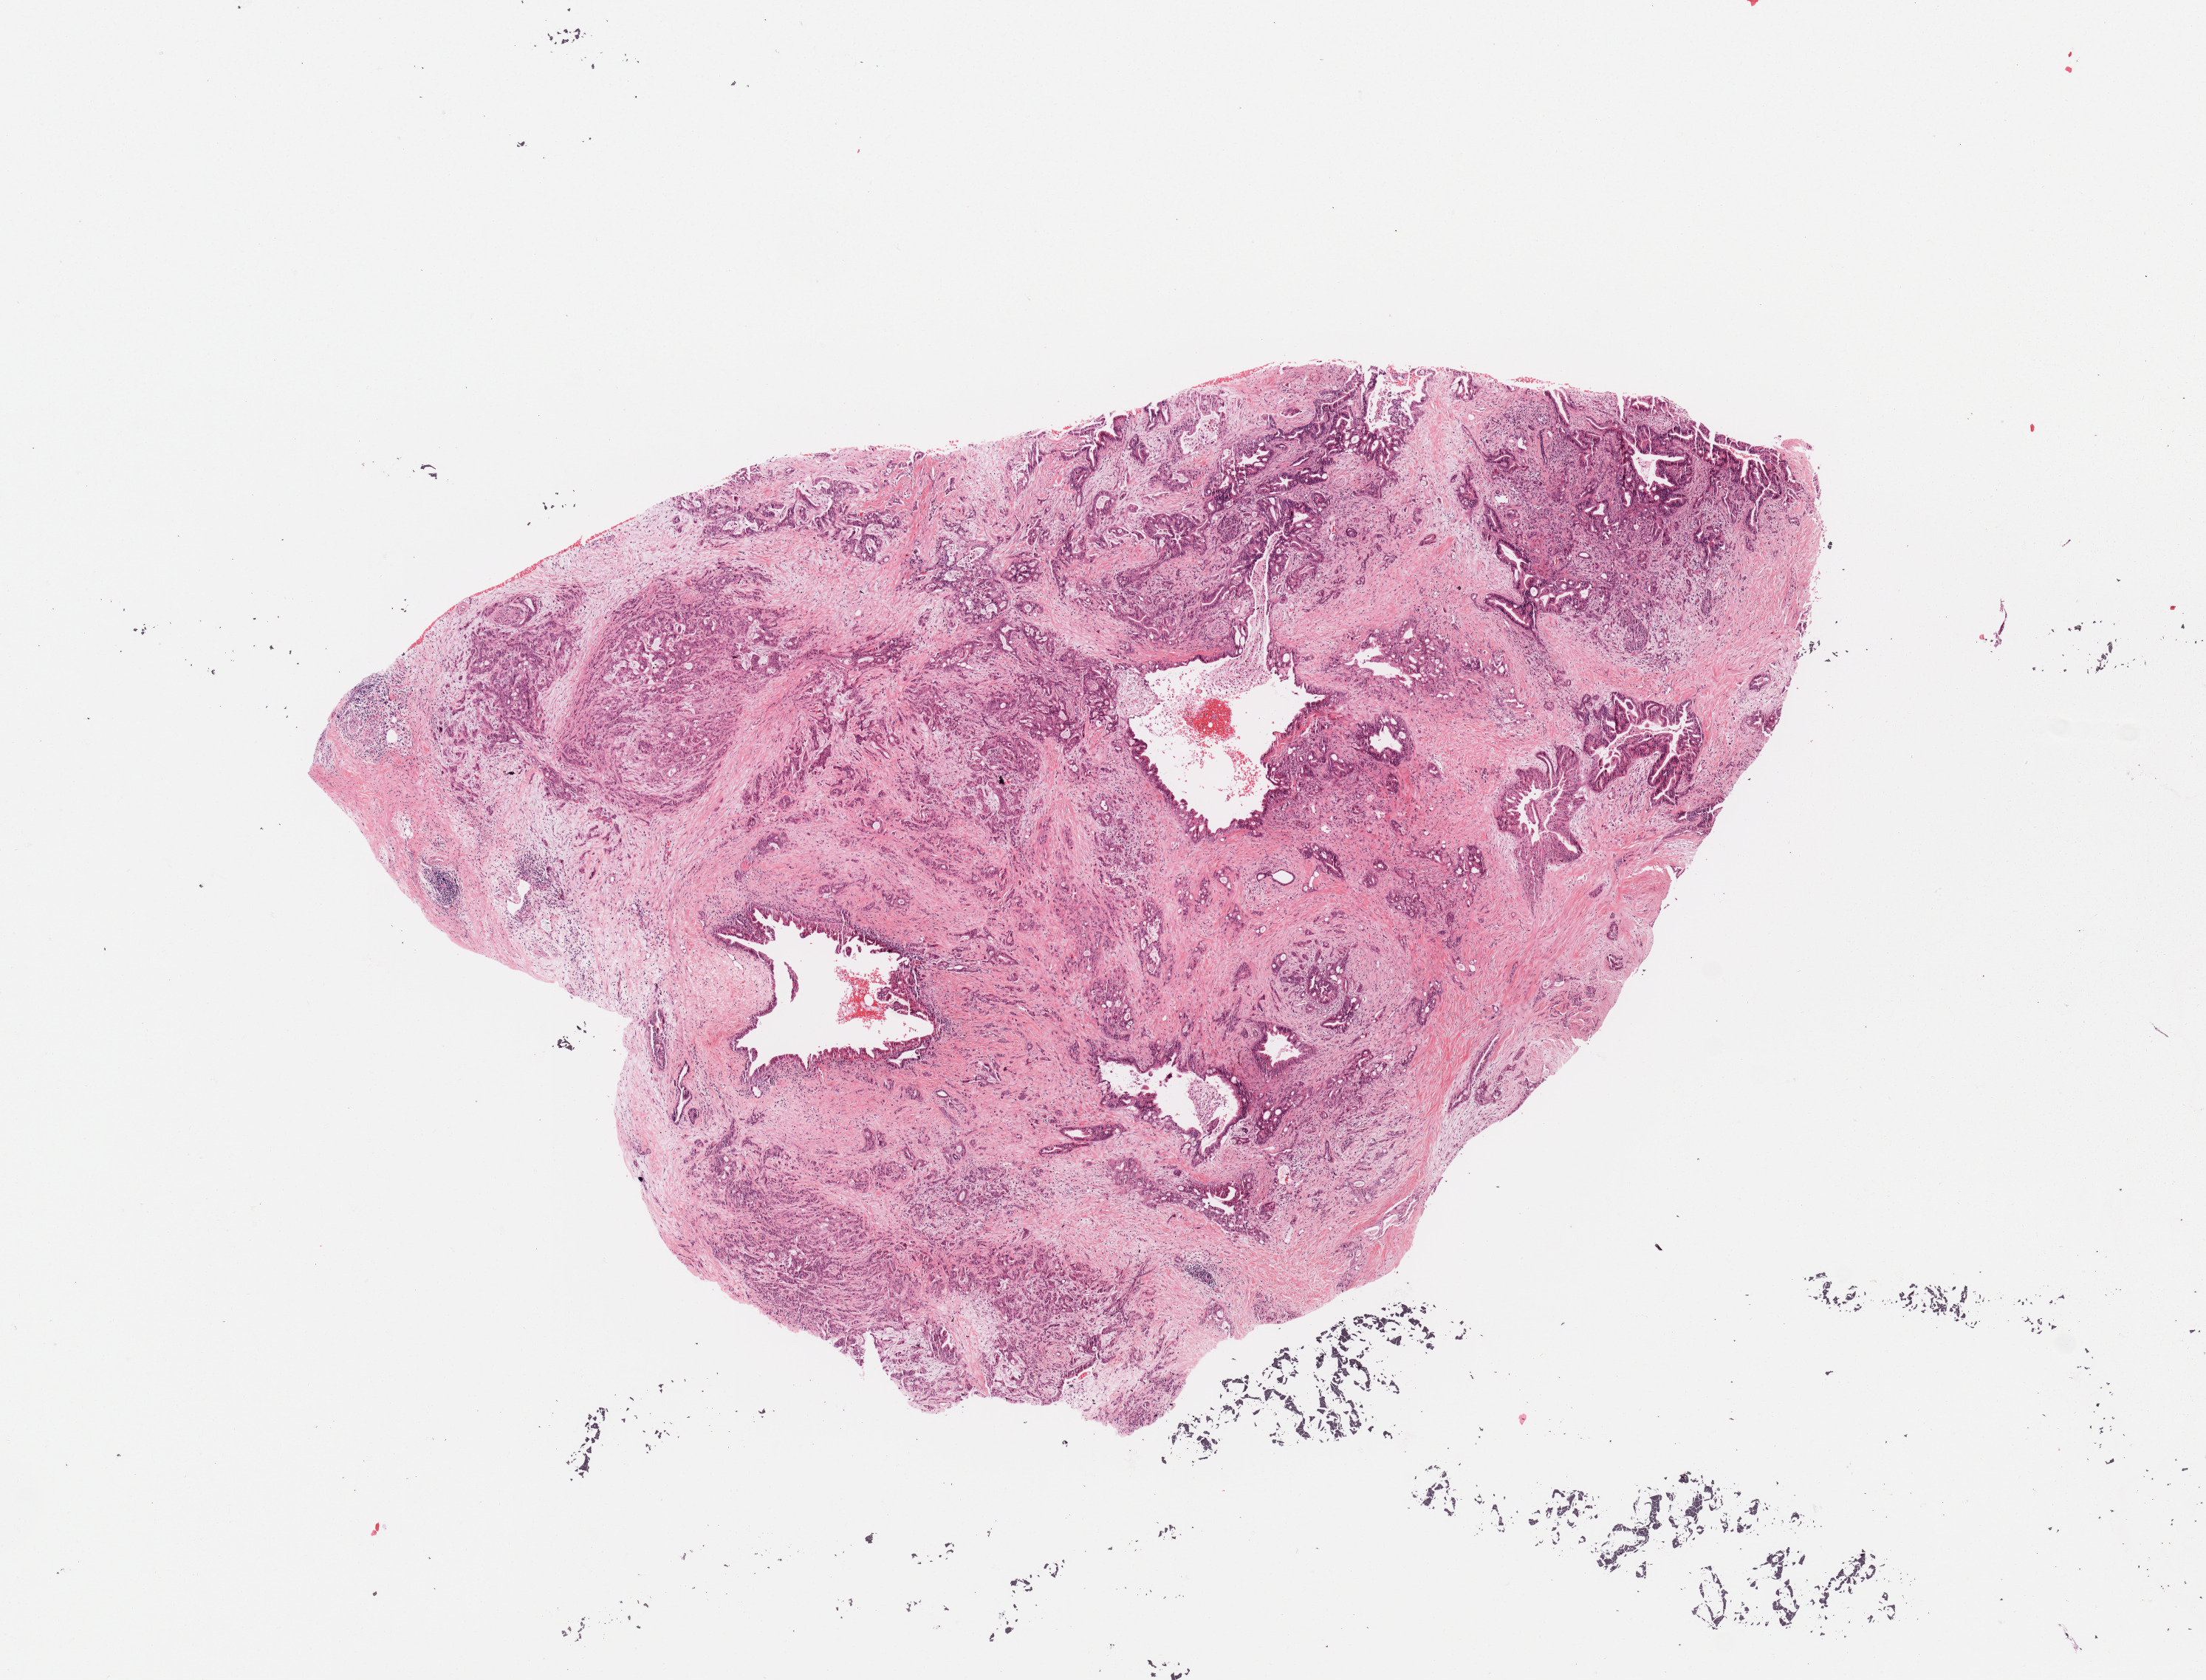
Hematoxylin and eosin (H&E) stained whole-slide image, a low-resolution overview of the entire scanned area, about 11.8 x 9.0 mm (acquisition: 20x scan), tumour tissue sample, sampled site: pancreas. 65-year-old male patient. Histologic grade: G3 (poorly differentiated). Pathologist review of this section (percent, as recorded): tumour nuclei 70%, necrosis 2%.
AJCC pathologic stage: IA. Diagnosis: Infiltrating duct carcinoma, NOS.